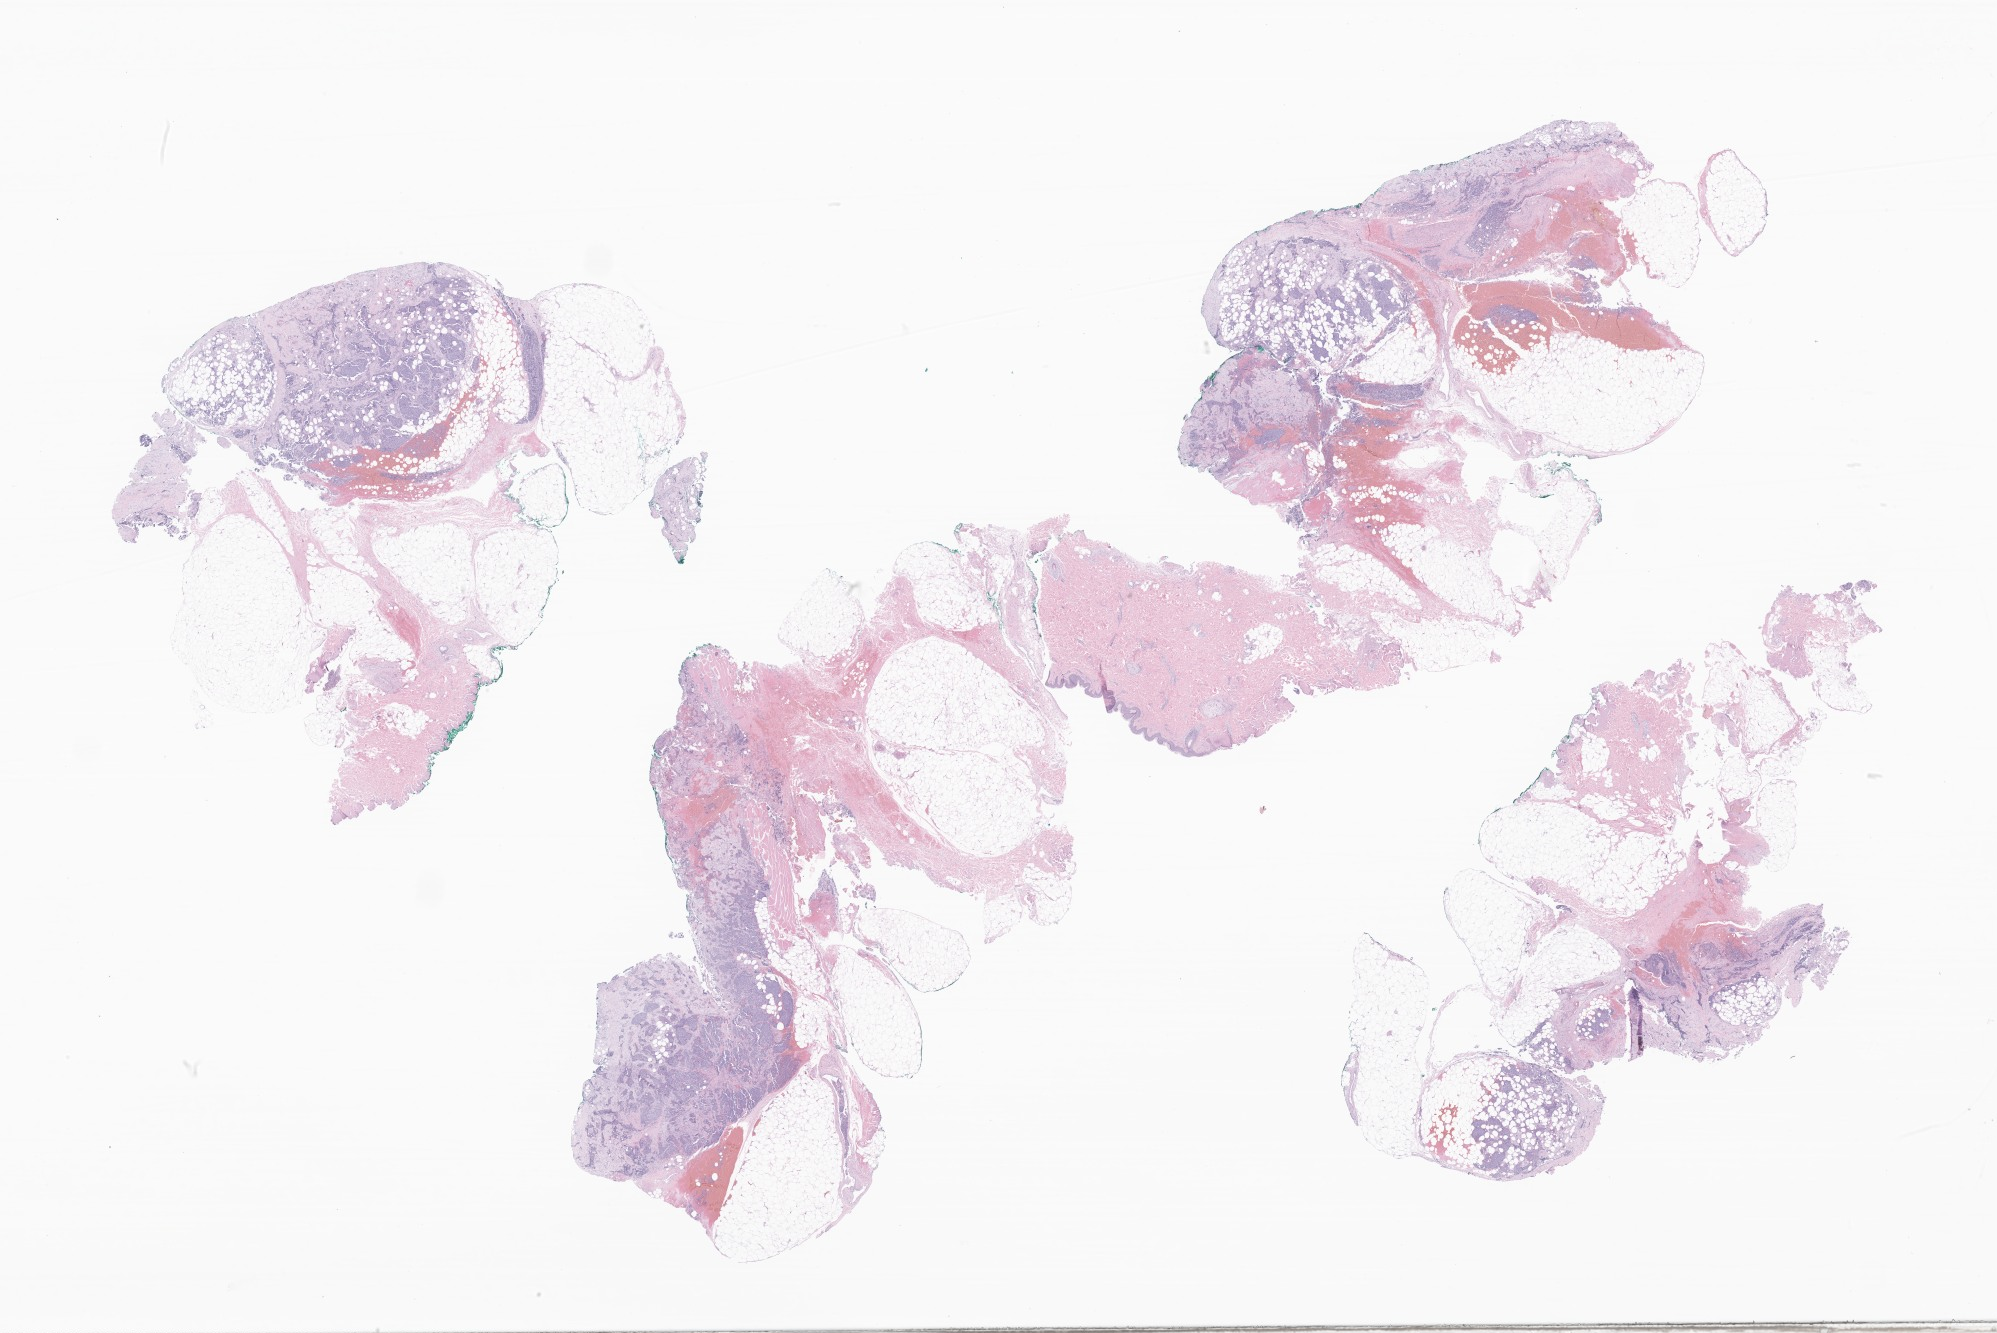
Hematoxylin and eosin (H&E) whole-slide image of tumor tissue from the lung, low-resolution overview of the scanned area, about 33.7 x 22.5 mm; formalin-fixed, paraffin-embedded (FFPE) tissue. Male patient, age 159 months.
Recorded diagnosis: Sarcoma, NOS.